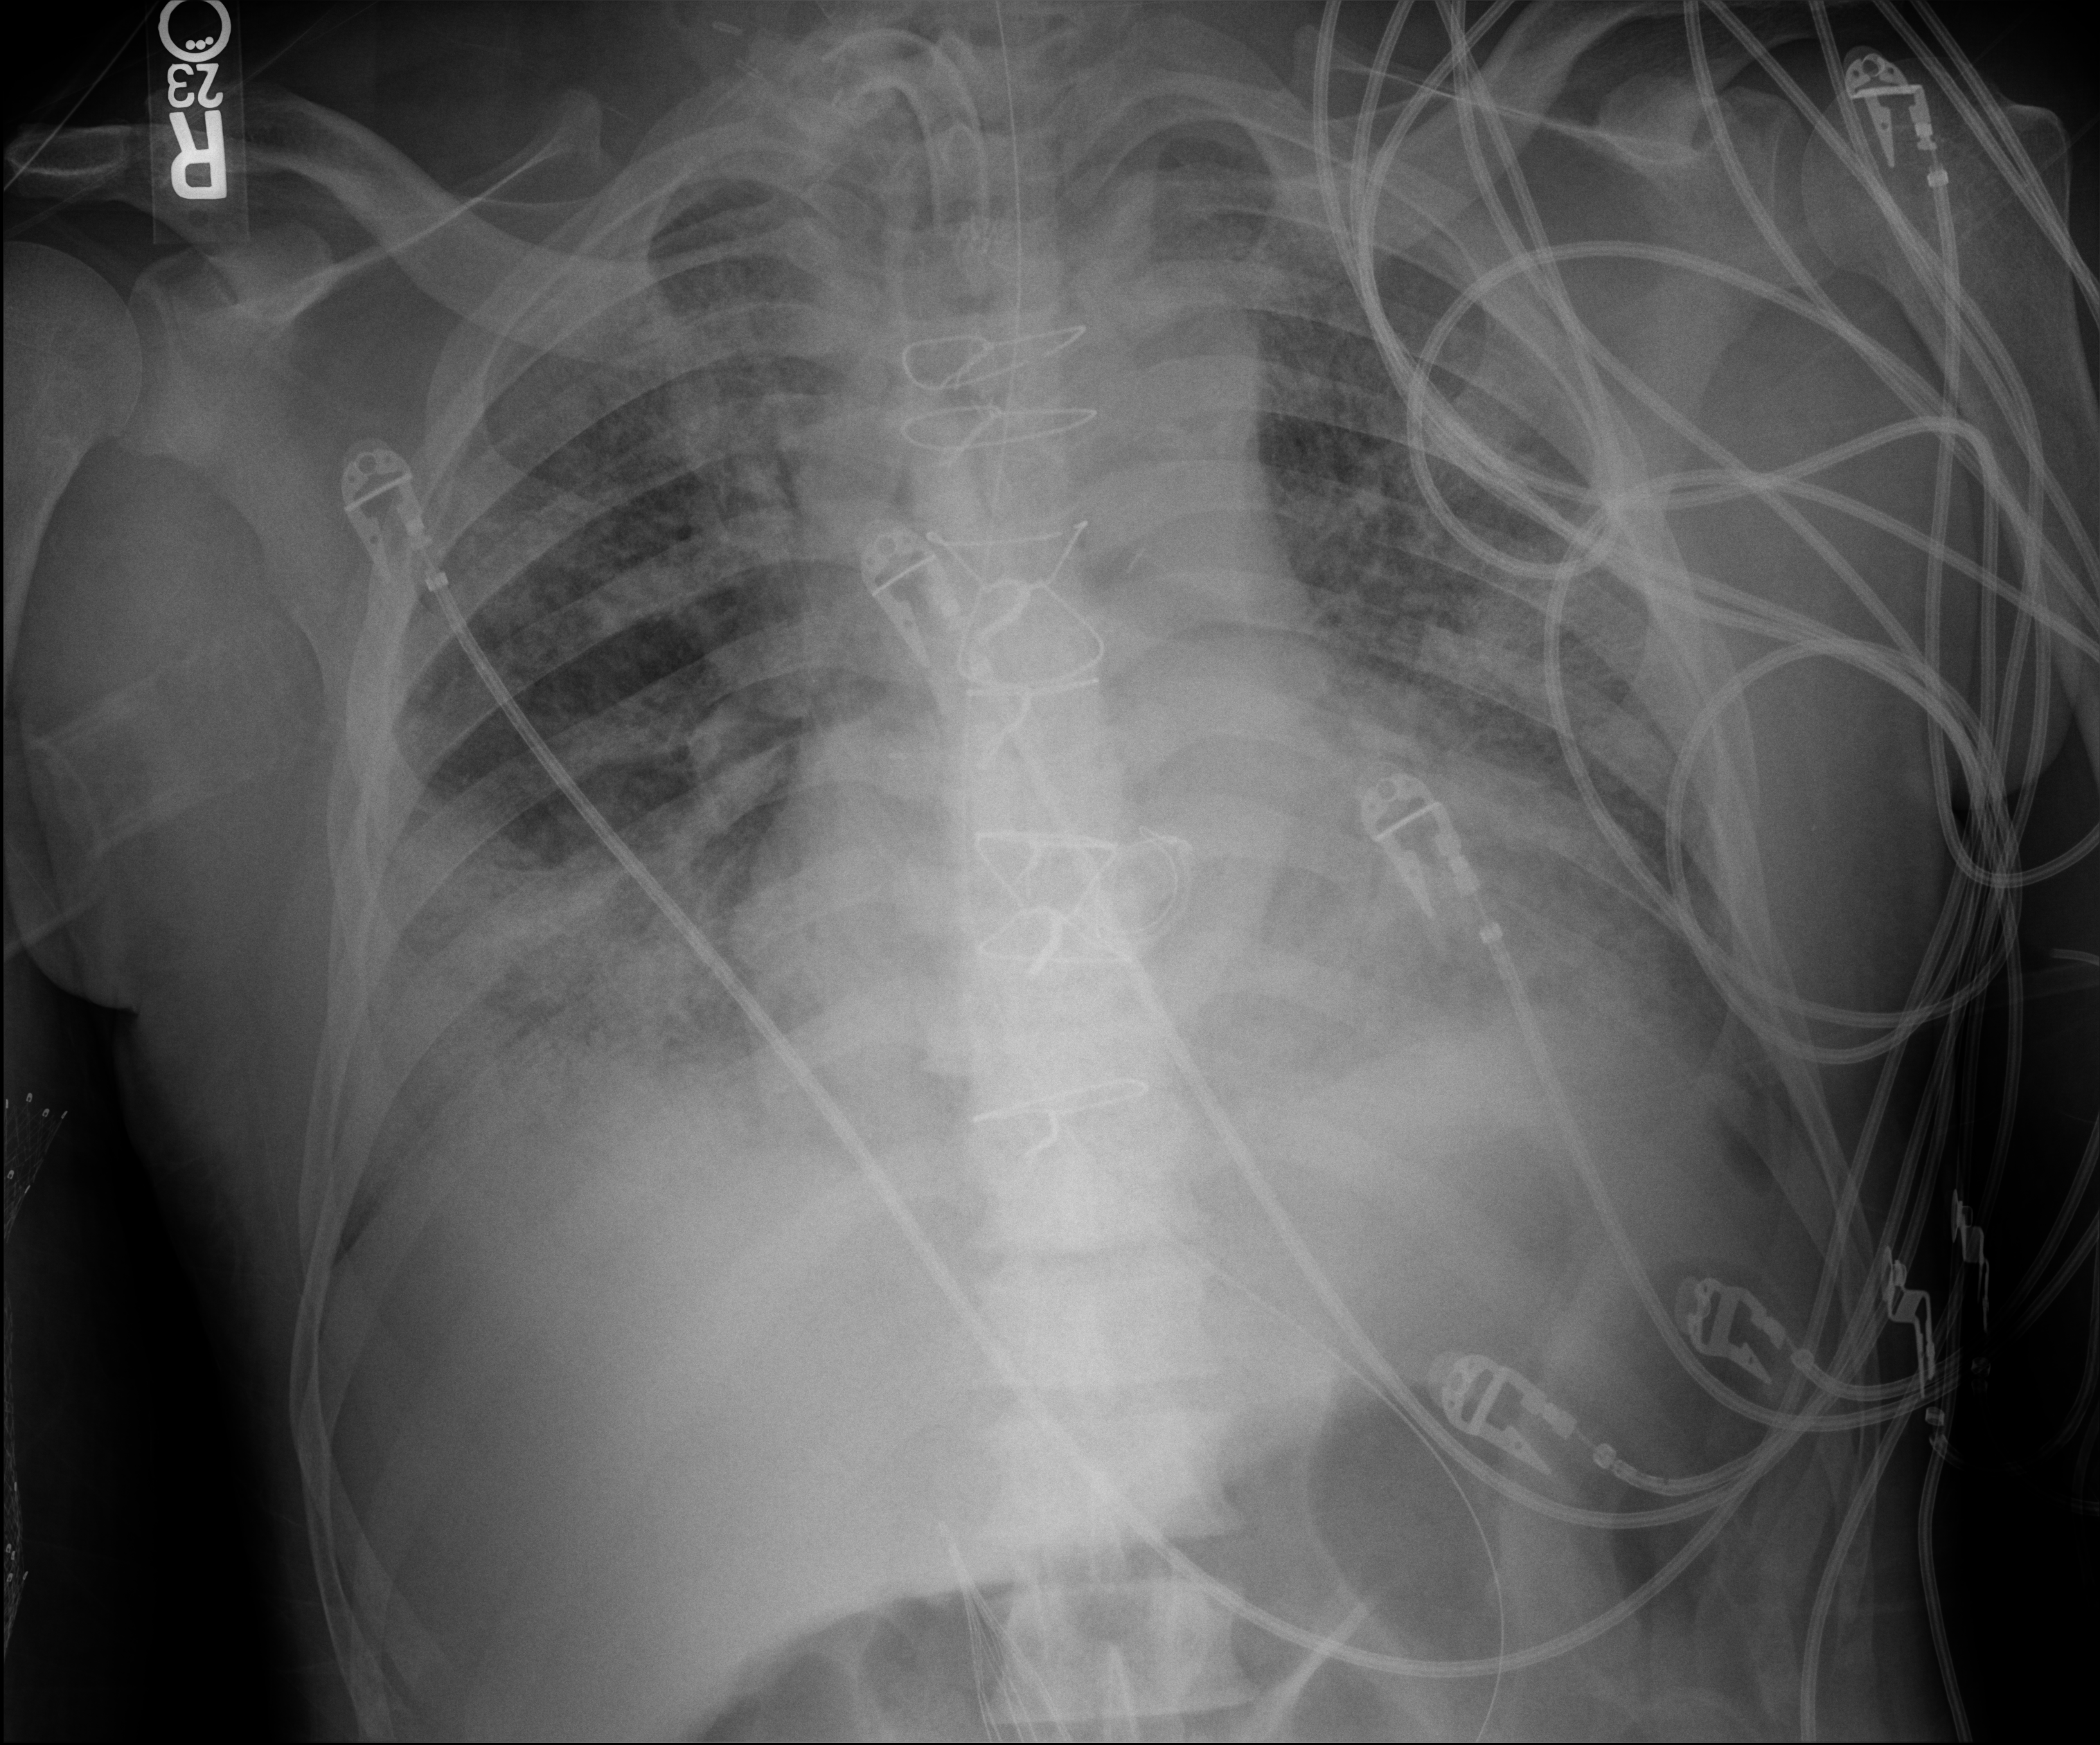
Portable chest radiograph. Male patient hospitalised with COVID-19, age 60–74 years.
From the hospital-stay record, not from the radiograph (when in the stay this image was taken is not recorded): COPD (admission record): no; chronic kidney disease (admission record): no; admitted to intensive care during this hospital stay: yes.